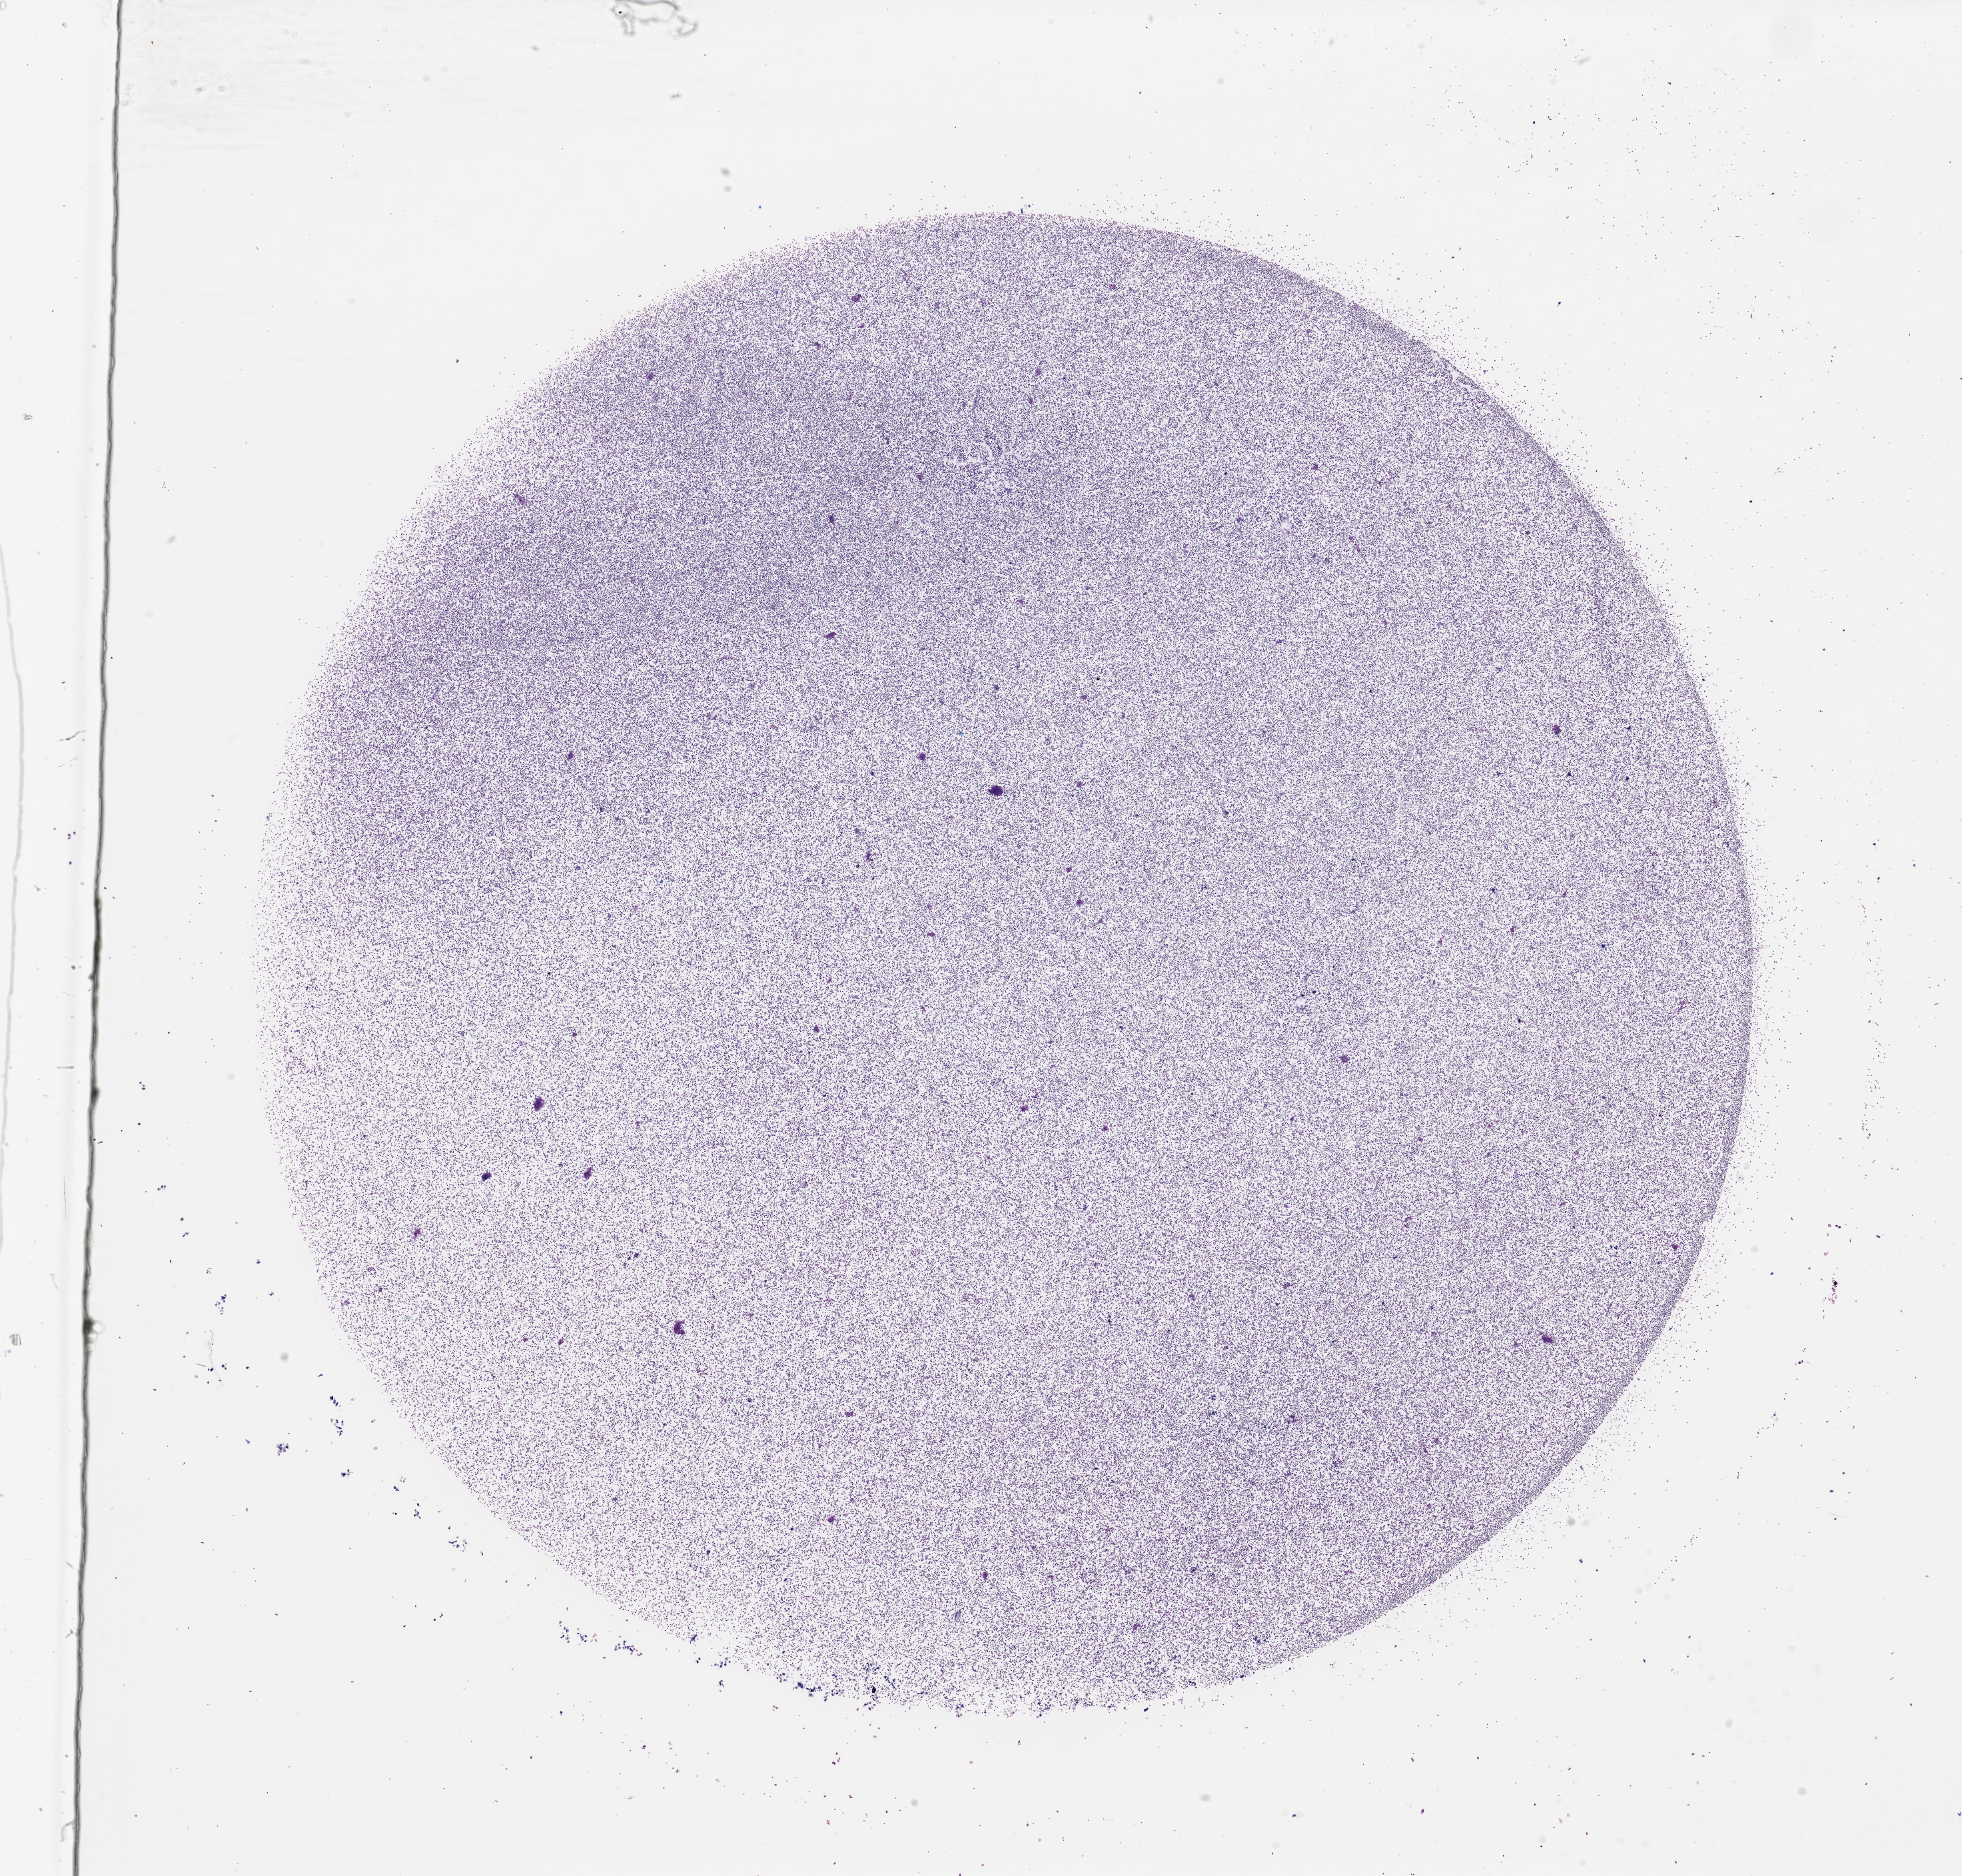
Whole-slide histology image, H&E — a low-resolution overview of the entire scanned area, about 23.3 x 22.2 mm (from a 40x scan). Bone marrow (leukaemic) sample. Patient: male, age 64 years.
Diagnosis: Acute Myeloid Leukemia.